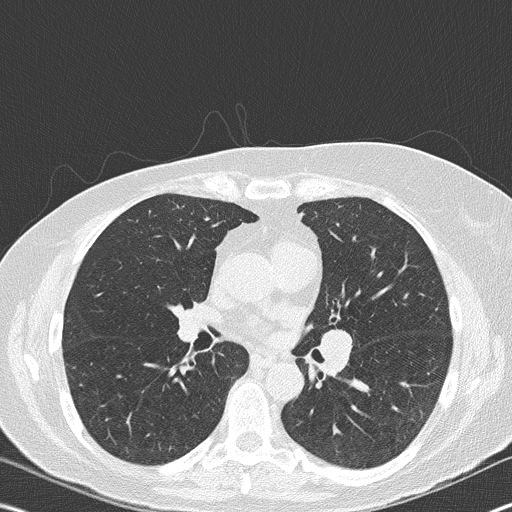
Low-dose screening chest CT, one axial slice. Position 97 of 177 along the scan axis. Reconstruction kernel B50f. 120 kVp. Lung window (W 1500 / L -600 HU). 512 × 512 image matrix, field of view 342 × 342 mm.
Outlined on this slice (outlined manually by an expert reader):
- lesion 2 (nodule, hilum of left lung): bounding box <321,329,354,373> (left, top, right, bottom; pixels)